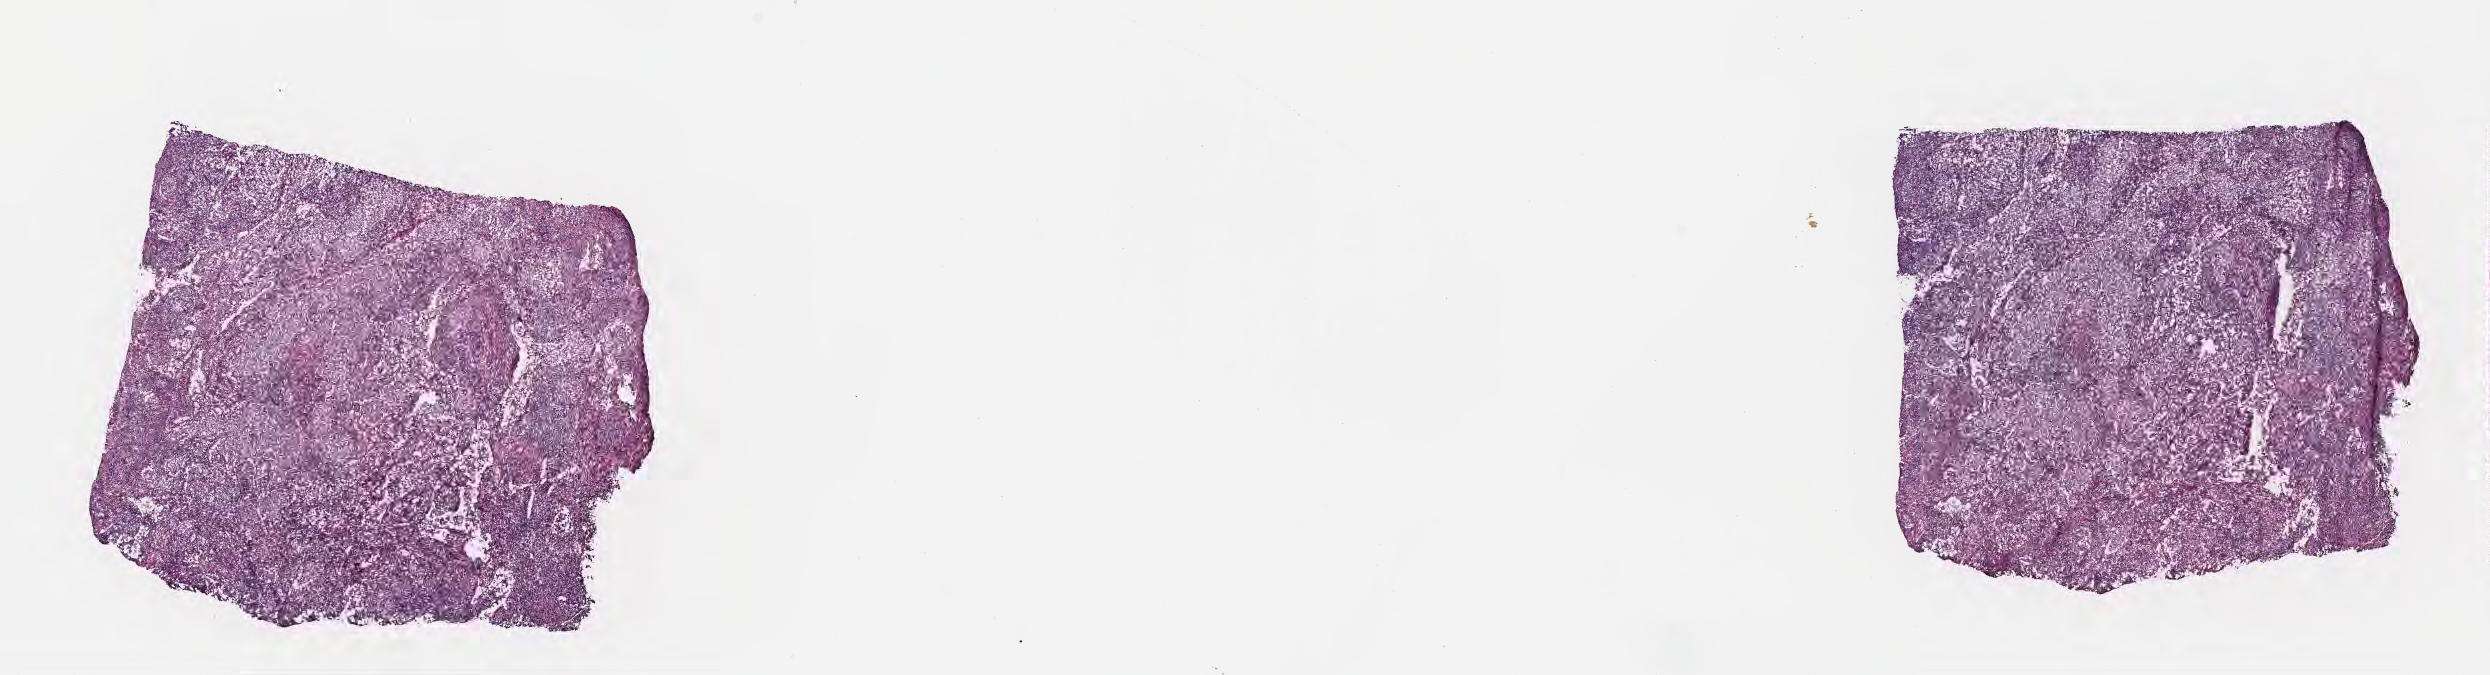
Whole-slide image, hematoxylin and eosin (H&E) stain, low-resolution overview of the scanned area, about 20.1 x 5.5 mm. Frozen section (tissue freezing medium). Primary tumor. Site: middle lobe of right lung. Patient male; aged 54. Composition of this section per pathologist review: tumor cells 60%, tumor nuclei 70%, stromal cells 40%, necrosis 0%, normal cells 0%. Inflammatory infiltration, as recorded: lymphocyte infiltration 80%, monocyte infiltration 20%, neutrophil infiltration 0%.
• histologic diagnosis: Clear cell adenocarcinoma, NOS
• AJCC pathologic stage: Stage IIA